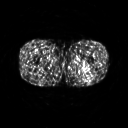
FDG PET of an extremity soft-tissue mass (from a PET/CT study), one axial slice. Slice 235 of 267 in the series (ordered by position). 3.27 mm slice thickness. 128 × 128 image matrix, field of view 500 × 500 mm. Patient: male, 27 years. Case-level facts recorded for this patient, not image findings: histological type: extraskeletal osteosarcoma; grade: high; site of the primary tumour: left adductur.
Outlined on this slice (expert contour drawn on MRI and transferred to this co-registered scan by the dataset authors):
- gross tumour volume (mass): box from (x=68, y=60) to (x=95, y=74) px